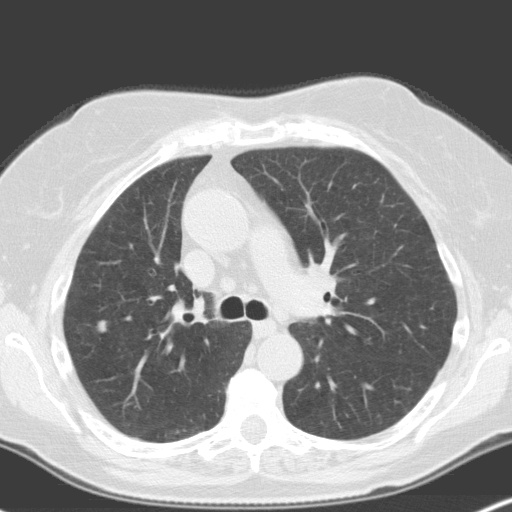
Low-dose screening chest CT, one axial slice; slice 113 of 160 in the series (ordered by position); lung window (W 1500 / L -600 HU); 3.2 mm slice thickness; 512 × 512 image matrix.
Outlined on this slice (outlined manually by an expert reader):
- lesion 3 (nodule): bounding box (x1, y1, x2, y2) in pixels: (99, 321, 107, 331)